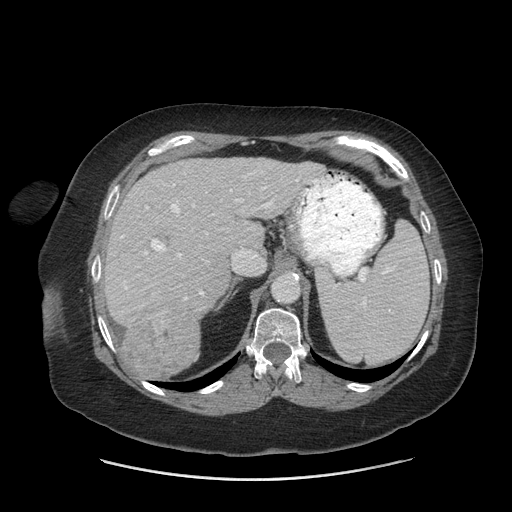
Contrast-enhanced abdominal CT (liver protocol), one axial slice. Slice 48 of 69 in the series (ordered by position). 140 kVp. Soft-tissue window (W 400 / L 40 HU). 512 × 512 image matrix, field of view 420 × 420 mm. Case-level facts recorded for this patient, not image findings: diagnosis: hepatocellular carcinoma (patient treated with transarterial chemoembolisation; whether this scan precedes or follows treatment is not stated here); TNM stage (as recorded): Stage-IIIB; Child-Pugh class: A; tumour differentiation: moderately differentiated; tumour nodularity: multinodular.
Outlined on this slice (semi-automatic segmentation, software-assisted and operator-edited):
- liver parenchyma outside the tumour (the mass and vessels are separate outlines, so this box may not span the whole liver): bounding box [x1, y1, x2, y2] px = [102, 158, 324, 340]
- mass: [122, 299, 200, 380]
- liver vessels: [121, 171, 298, 300]